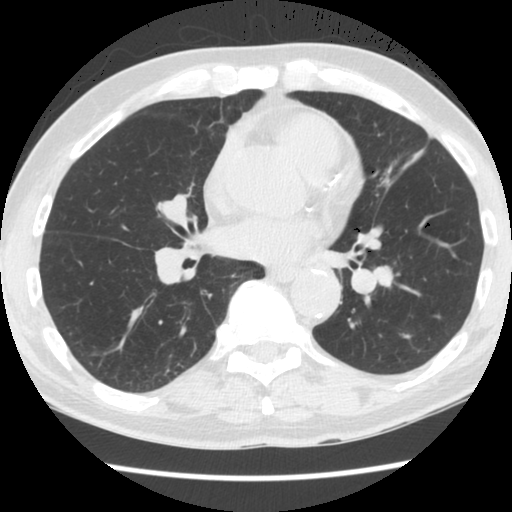
Low-dose screening chest CT, one axial slice; position 76 of 174 along the scan axis; reconstruction kernel STANDARD; 120 kVp; lung window (W 1500 / L -600 HU); 2.5 mm slice thickness; 512 × 512 image matrix, field of view 320 × 320 mm.
Outlined on this slice (manually delineated by an expert):
- lesion 1 (tumor, lower lobe of left lung): bounding box (x1, y1, x2, y2) in pixels: (374, 267, 392, 286)